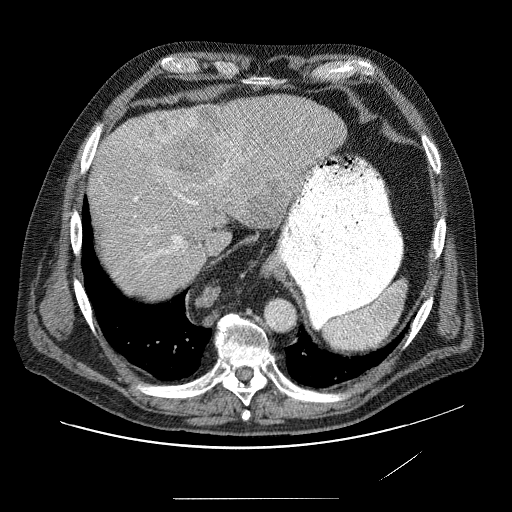
Contrast-enhanced abdominal CT (liver protocol), one axial slice; position 65 of 89 along the scan axis; 120 kVp; soft-tissue window (W 400 / L 40 HU); 2.5 mm slice thickness; 512 × 512 image matrix, field of view 420 × 420 mm. From the clinical record (not read from this slice): diagnosis: hepatocellular carcinoma (patient treated with transarterial chemoembolisation; whether this scan precedes or follows treatment is not stated here); TNM stage (as recorded): Stage-IVA; Child-Pugh class: A; tumour differentiation: moderately differentiated; tumour nodularity: multinodular.
Annotated regions visible in this slice (semi-automatic segmentation, software-assisted and operator-edited):
- liver parenchyma outside the tumour (the mass and vessels are separate outlines, so this box may not span the whole liver): bounding box [x1, y1, x2, y2] px = [88, 96, 346, 280]
- mass: [146, 107, 304, 222]
- liver vessels: [130, 131, 219, 261]